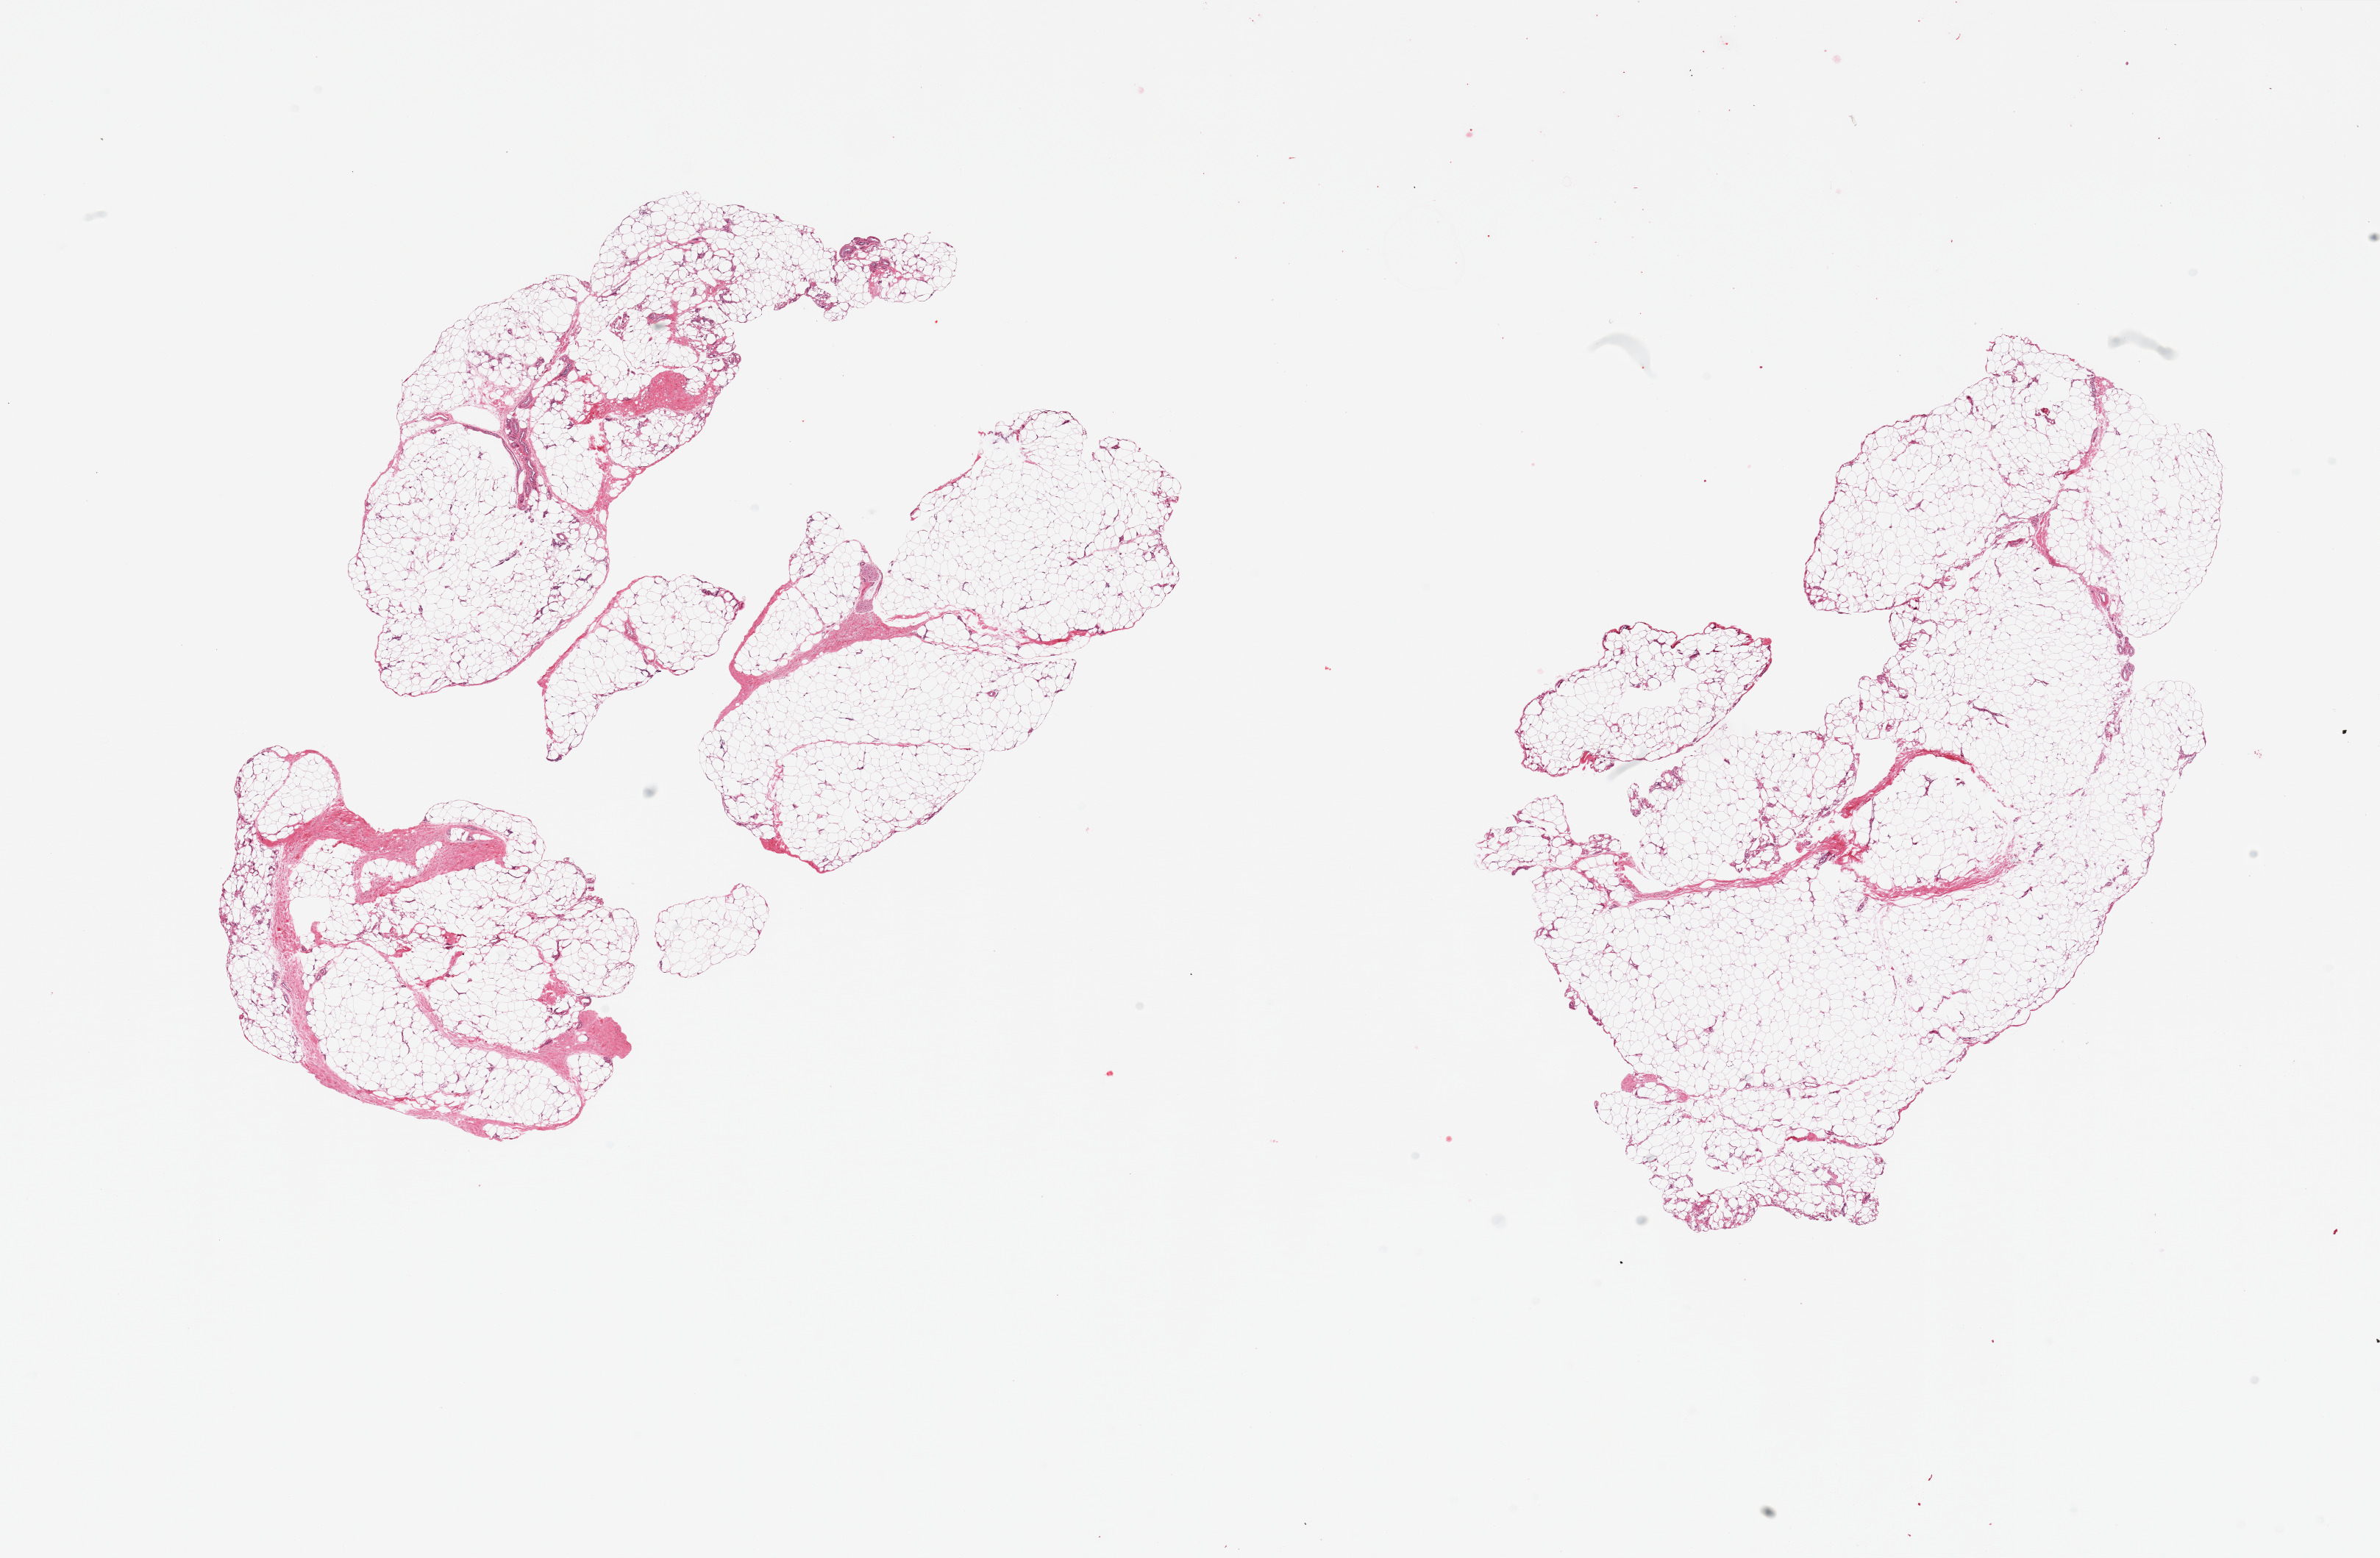
H&E whole-slide image — shown as a low-resolution overview of the whole scanned area (about 25.6 x 16.8 mm), PAXgene-fixed paraffin-embedded (PFPE) section, section of adipose tissue (target tissue), donor tissue sample. Donor sex: female.
Pathologist's review note for this sample: 2 pieces, ~5-10 % fascia.